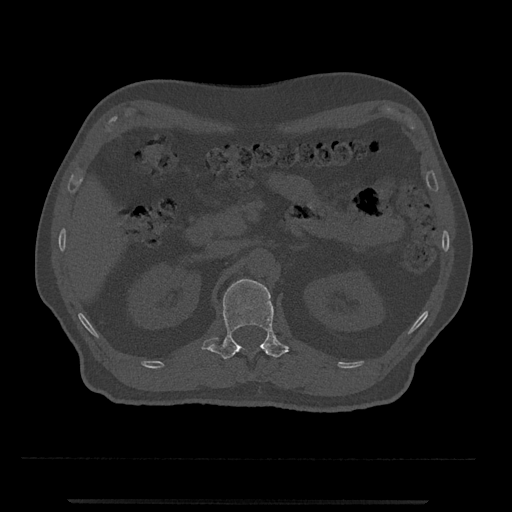
CT including the spine, one axial slice. Slice 345 of 797 in the series (ordered by position). Reconstruction kernel Br40s/3. 120 kVp. Bone window (W 1800 / L 400 HU). 512 × 512 image matrix, field of view 419 × 419 mm. Male patient, age 63 years. Case-level facts recorded for this patient, not image findings: primary cancer: prostate.
Structures marked on this image (semi-automatic segmentation, software-assisted and operator-edited):
- L1 vertebra: box from (x=201, y=279) to (x=293, y=359) px